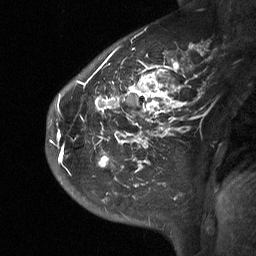
Breast MRI (dynamic contrast-enhanced), one sagittal slice; dynamic contrast-enhanced study with each time point stored as its own series, time point 2 of 3 at this slice position (early post-contrast, ordered by acquisition time); 1.5 T; TE 4.8 ms, TR 27 ms; 2 mm slice thickness; 256 × 256 image matrix, field of view 200 × 200 mm. Female patient, age 42 years. Case-level facts recorded for this patient, not image findings: setting: breast cancer imaged before/during neoadjuvant chemotherapy; receptor status: triple-negative.
Structures marked on this image (semi-automatic segmentation, software-assisted and operator-edited):
- analysis volume of interest (the breast-tissue region the enhancement analysis was run in; not a lesion): bounding box [x1, y1, x2, y2] px = [46, 29, 203, 190]
- tumour enhancement mask (voxels above the 90 % enhancement threshold inside the analysis volume of interest): [50, 49, 184, 167]